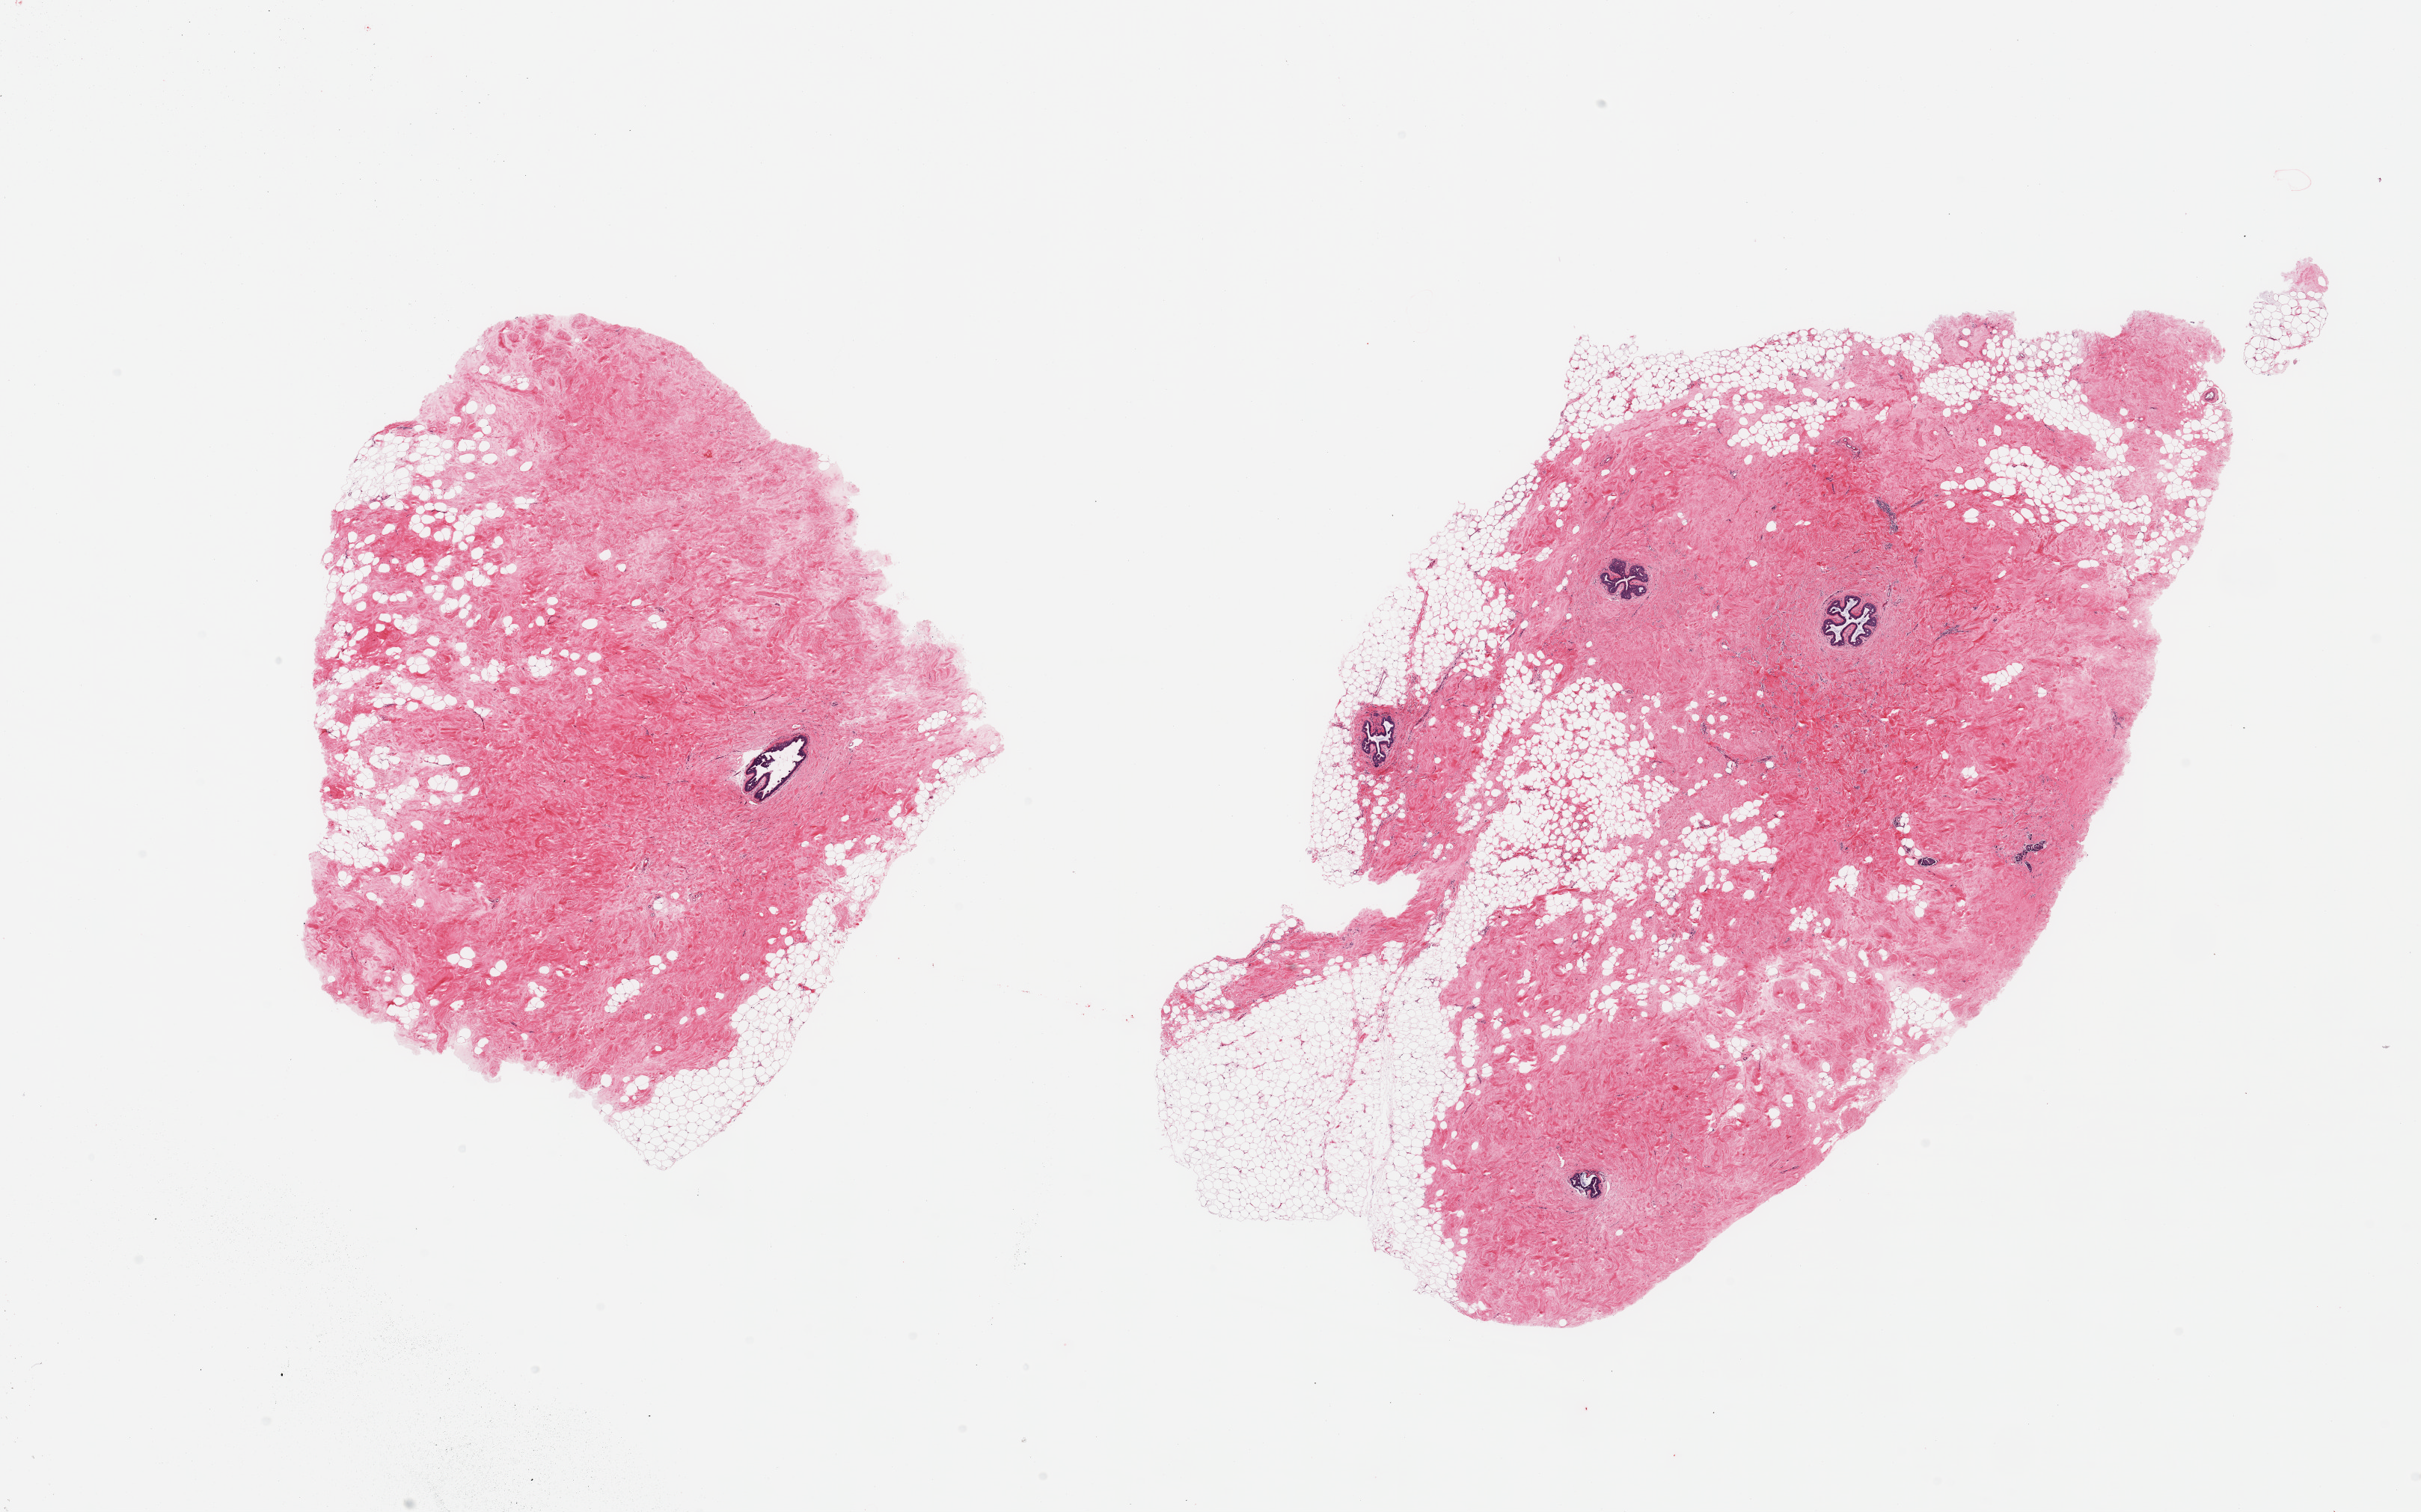
Whole-slide image, H&E stain — shown as a low-resolution overview of the whole scanned area (about 25.6 x 16.0 mm). PAXgene-fixed, paraffin-embedded tissue. Target tissue: breast. Donor tissue sample. Female donor.
Reviewer comment on this tissue sample: 2 pieces; fat (20 and 40%) and dense fibrocollagenous stroma with scattered epithelial component, focal simple hyperplasia.